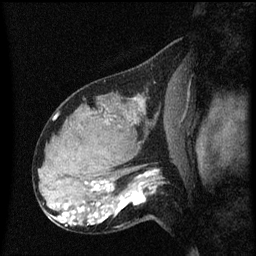
Breast MRI (dynamic contrast-enhanced), one sagittal slice; slice 36 of 60 in the series (ordered by position); dynamic contrast-enhanced series, image 2 of 3 at this slice position (ordered by acquisition); 1.5 T; TE 4.2 ms, TR 8.4 ms; 256 × 256 image matrix, field of view 200 × 200 mm. Female patient, age 31 years. Case-level facts recorded for this patient, not image findings: setting: breast cancer imaged before/during neoadjuvant chemotherapy; receptor status: HR-positive, HER2-negative.
Outlined on this slice (semi-automatic segmentation, software-assisted and operator-edited):
- analysis volume of interest (the breast-tissue region the enhancement analysis was run in; not a lesion): bounding box (x1, y1, x2, y2) in pixels: (102, 166, 167, 223)
- tumour enhancement mask (voxels above the 70 % enhancement threshold inside the analysis volume of interest): (102, 172, 157, 223)